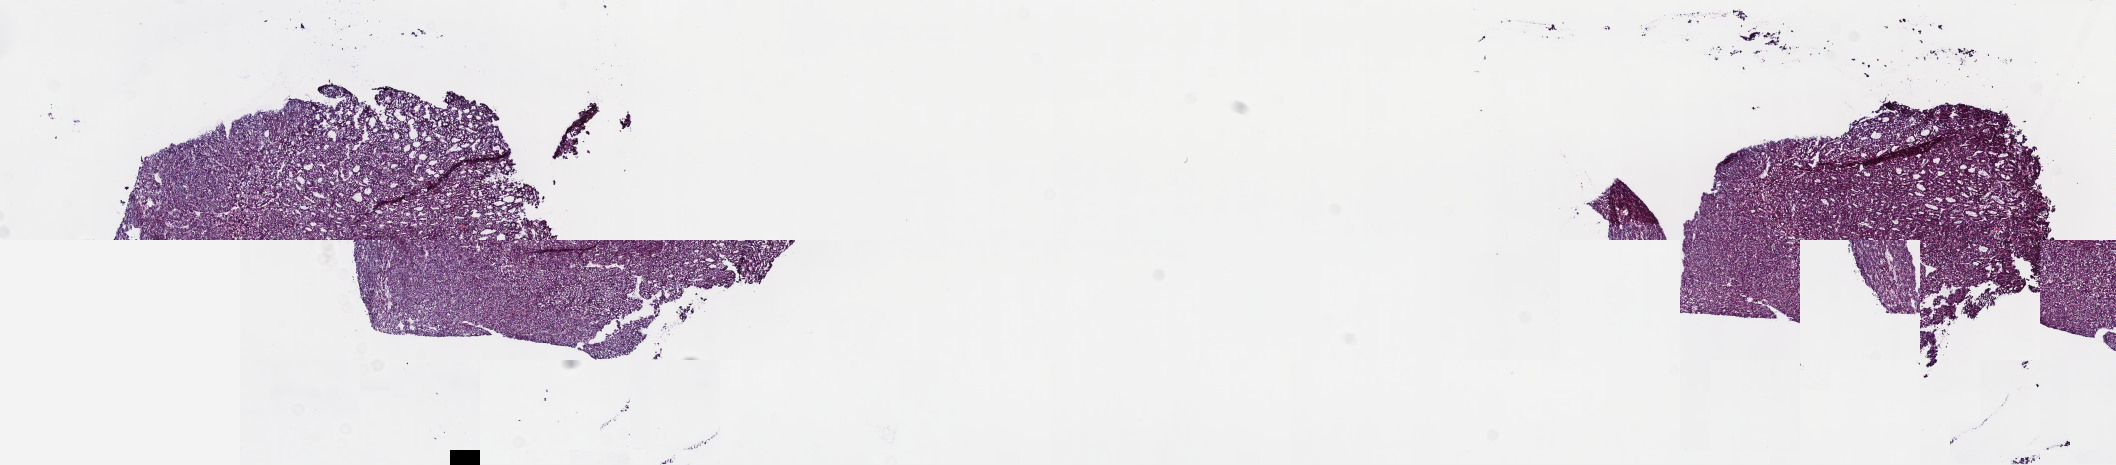
Hematoxylin and eosin (H&E) stained whole-slide image, shown as a low-resolution overview of the whole scanned area (about 17.1 x 3.8 mm), frozen section from the top of the tissue portion, liver, primary tumour sample. Male patient; age at initial diagnosis 70 years. Histologic grade: G2 (moderately differentiated). Pathologist review of this section (percent, as recorded): tumour cells 95%, tumour nuclei 96%, normal cells 0%, stromal cells 3%, necrosis 2%. Infiltration values recorded for this section: lymphocyte infiltration 3%, monocyte infiltration 0%, neutrophil infiltration 0%.
- AJCC pathologic stage: I
- diagnosis: Hepatocellular carcinoma, NOS